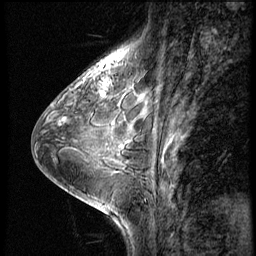
Breast MRI (dynamic contrast-enhanced), one sagittal slice; position 21 of 56 along the scan axis; 4 images stored at this slice position (order not interpretable as contrast timing); 1.5 T; TE 4.2 ms, TR 8.9 ms; 2.5 mm slice thickness; 256 × 256 image matrix, field of view 200 × 200 mm. Female patient, age 38 years. From the clinical record (not read from this slice): setting: breast cancer imaged before/during neoadjuvant chemotherapy; receptor status: triple-negative.
Outlined on this slice (semi-automatic segmentation, software-assisted and operator-edited):
- analysis volume of interest (the breast-tissue region the enhancement analysis was run in; not a lesion): bounding box <88,73,115,102> (left, top, right, bottom; pixels)
- tumour enhancement mask (voxels above the 140 % enhancement threshold inside the analysis volume of interest): <102,84,107,97>